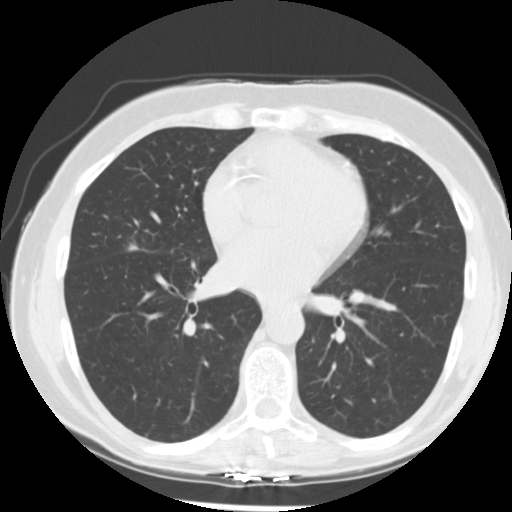
Low-dose screening chest CT, one axial slice; position 126 of 255 along the scan axis; lung window (W 1500 / L -600 HU); 2.5 mm slice thickness; 512 × 512 image matrix.
Structures marked on this image (expert manual segmentation):
- lesion 1 (tumor, middle lobe of right lung): box from (x=129, y=244) to (x=138, y=251) px